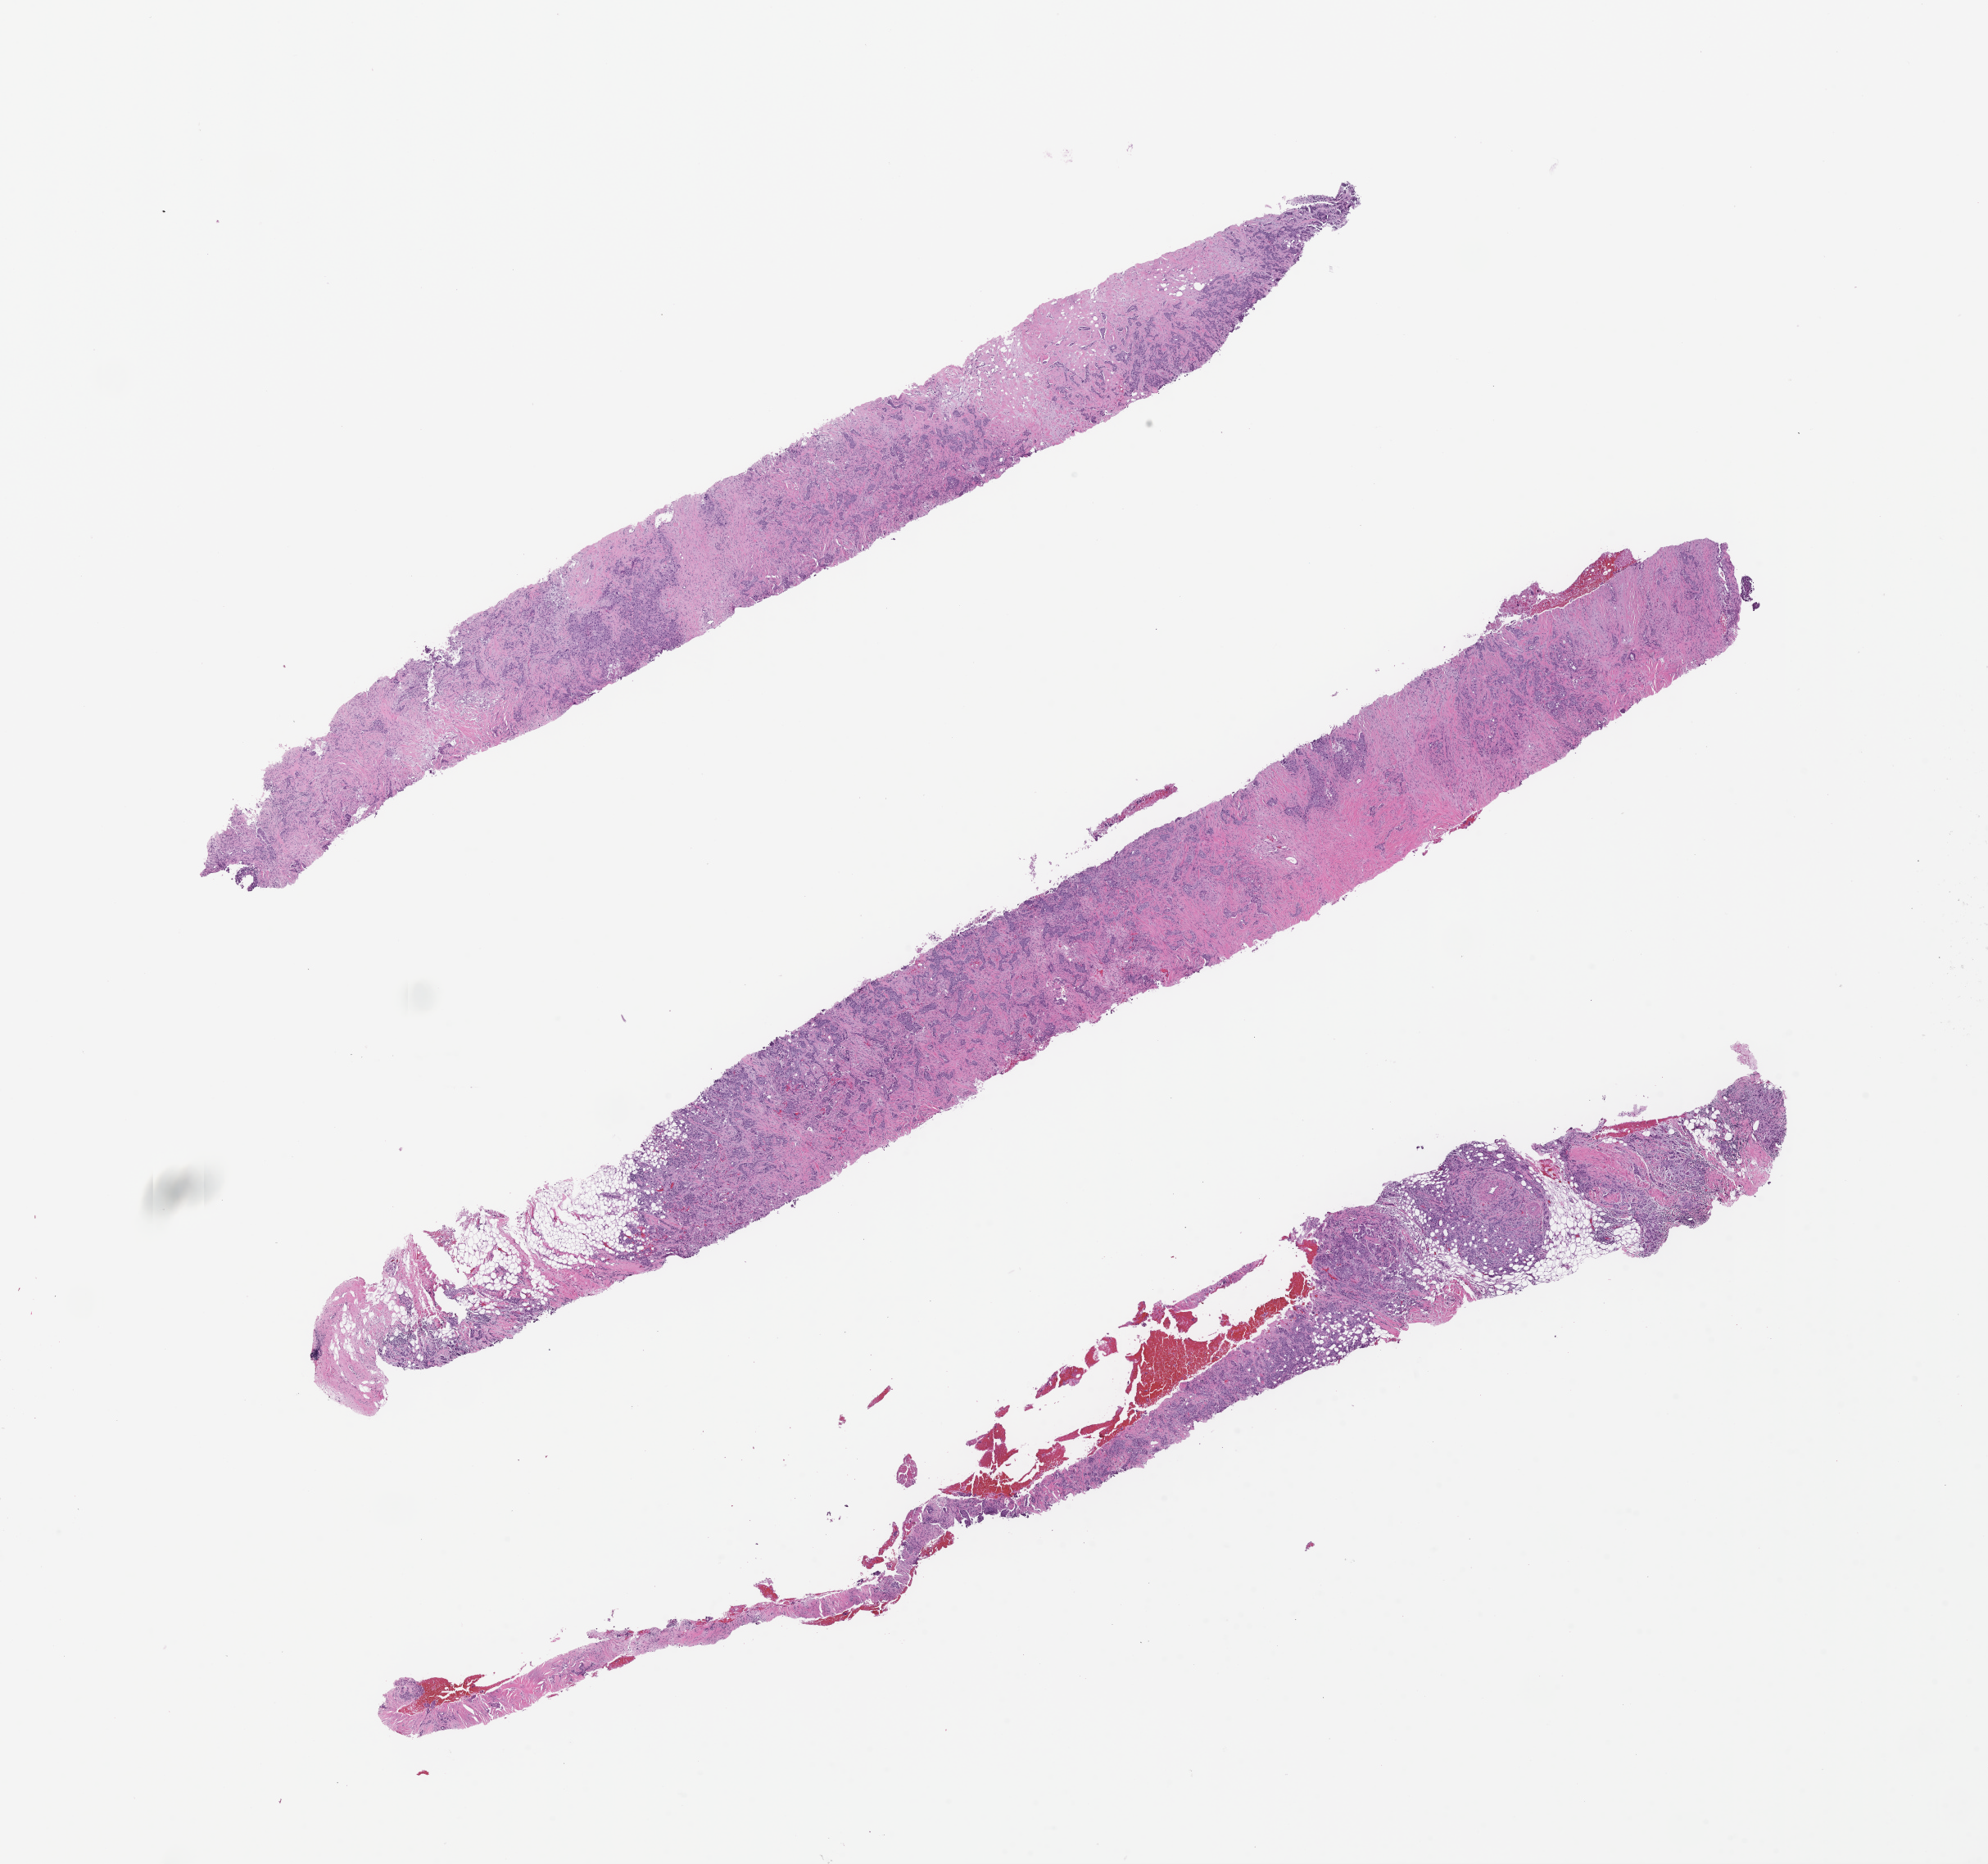
Whole-slide image, H&E stain — whole scanned area (about 19.6 x 18.4 mm) shown as a low-resolution overview; FFPE section; site: breast; specimen time point: archival tissue. Patient: female.
• this section: primary tumor
• diagnosis: Invasive Breast Carcinoma